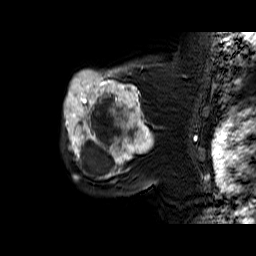
Breast MRI (dynamic contrast-enhanced), one sagittal slice; position 45 of 60 along the scan axis; dynamic contrast-enhanced series, time point 2 of 6 at this slice position (early post-contrast); 1.5 T; TE 6.4 ms, TR 32.9 ms; 4 mm slice thickness; 256 × 256 image matrix, field of view 200 × 200 mm. Female patient. From the clinical record (not read from this slice): setting: breast cancer imaged before/during neoadjuvant chemotherapy; receptor status: triple-negative.
Outlined on this slice (semi-automatic segmentation, software-assisted and operator-edited):
- analysis volume of interest (the breast-tissue region the enhancement analysis was run in; not a lesion): box from (x=63, y=65) to (x=159, y=174) px
- tumour enhancement mask (voxels above the 100 % enhancement threshold inside the analysis volume of interest): (x=64, y=65)–(x=154, y=174)